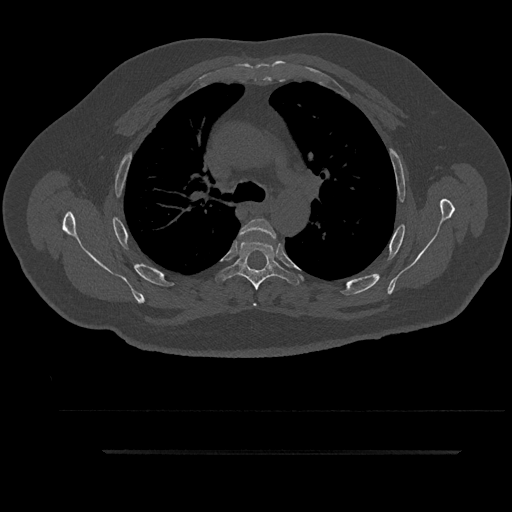
CT including the spine, one axial slice. Position 638 of 797 along the scan axis. Reconstruction kernel Br40s/3. 120 kVp. Bone window (W 1800 / L 400 HU). 0.5 mm slice thickness. 512 × 512 image matrix, field of view 432 × 432 mm. Patient: male, 63 years. From the clinical record (not read from this slice): primary cancer: renal; vertebrae with lytic lesions (as recorded): T8.
Structures marked on this image (semi-automatically segmented with operator editing):
- T4 vertebra: bounding box <238,218,278,306> (left, top, right, bottom; pixels)
- T5 vertebra: <216,240,299,290>